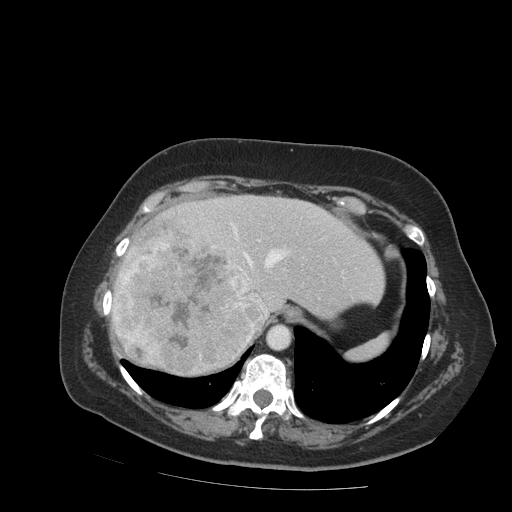
Contrast-enhanced abdominal CT (liver protocol), one axial slice; slice 69 of 99 in the series (ordered by position); reconstruction kernel STANDARD; 140 kVp; soft-tissue window (W 400 / L 40 HU); 2.5 mm slice thickness; 512 × 512 image matrix, field of view 400 × 400 mm. Case-level facts recorded for this patient, not image findings: diagnosis: hepatocellular carcinoma (patient treated with transarterial chemoembolisation; whether this scan precedes or follows treatment is not stated here); TNM stage (as recorded): Stage-IVB; Child-Pugh class: A.
Annotated regions visible in this slice (semi-automatically segmented with operator editing):
- abdominal aorta: bounding box [x1, y1, x2, y2] px = [267, 325, 290, 350]
- liver parenchyma outside the tumour (the mass and vessels are separate outlines, so this box may not span the whole liver): [114, 194, 384, 368]
- mass: [110, 225, 265, 377]
- liver vessels: [213, 223, 288, 326]